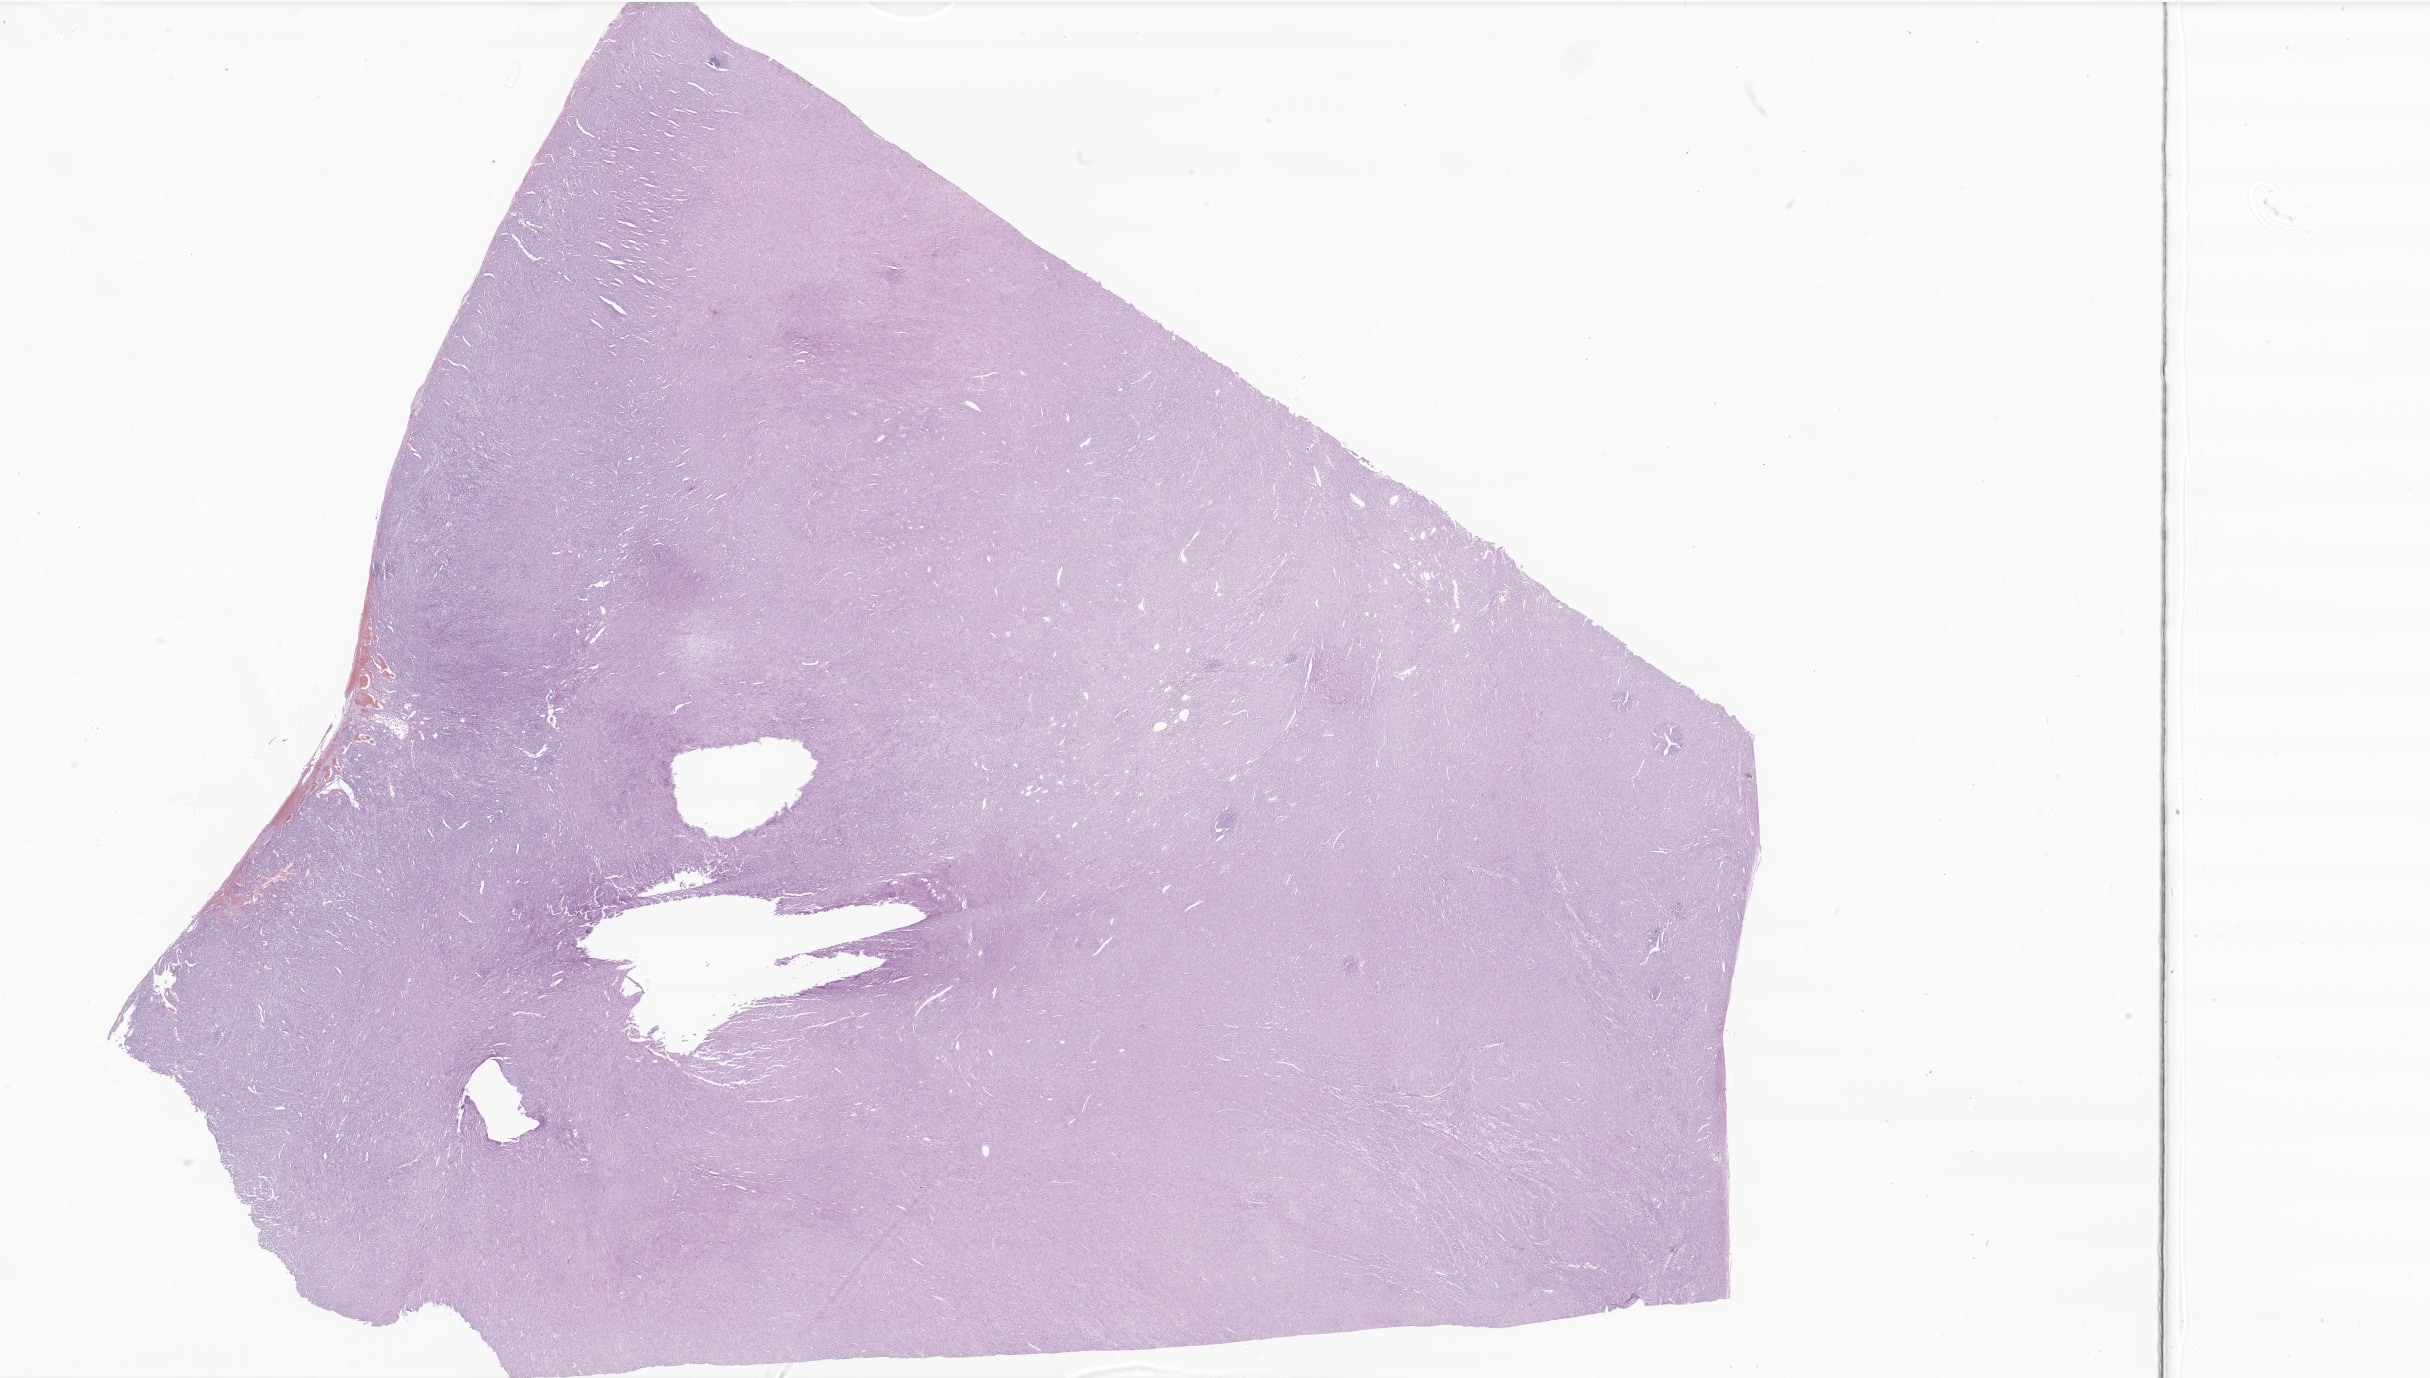
Digitized H&E-stained section of tumor tissue from the abdomen — whole scanned area (about 41.0 x 23.2 mm) shown as a low-resolution overview. Formalin-fixed, paraffin-embedded (FFPE) tissue. Patient female; age 556 days.
Diagnosis: Myofibroblastic tumor, NOS.